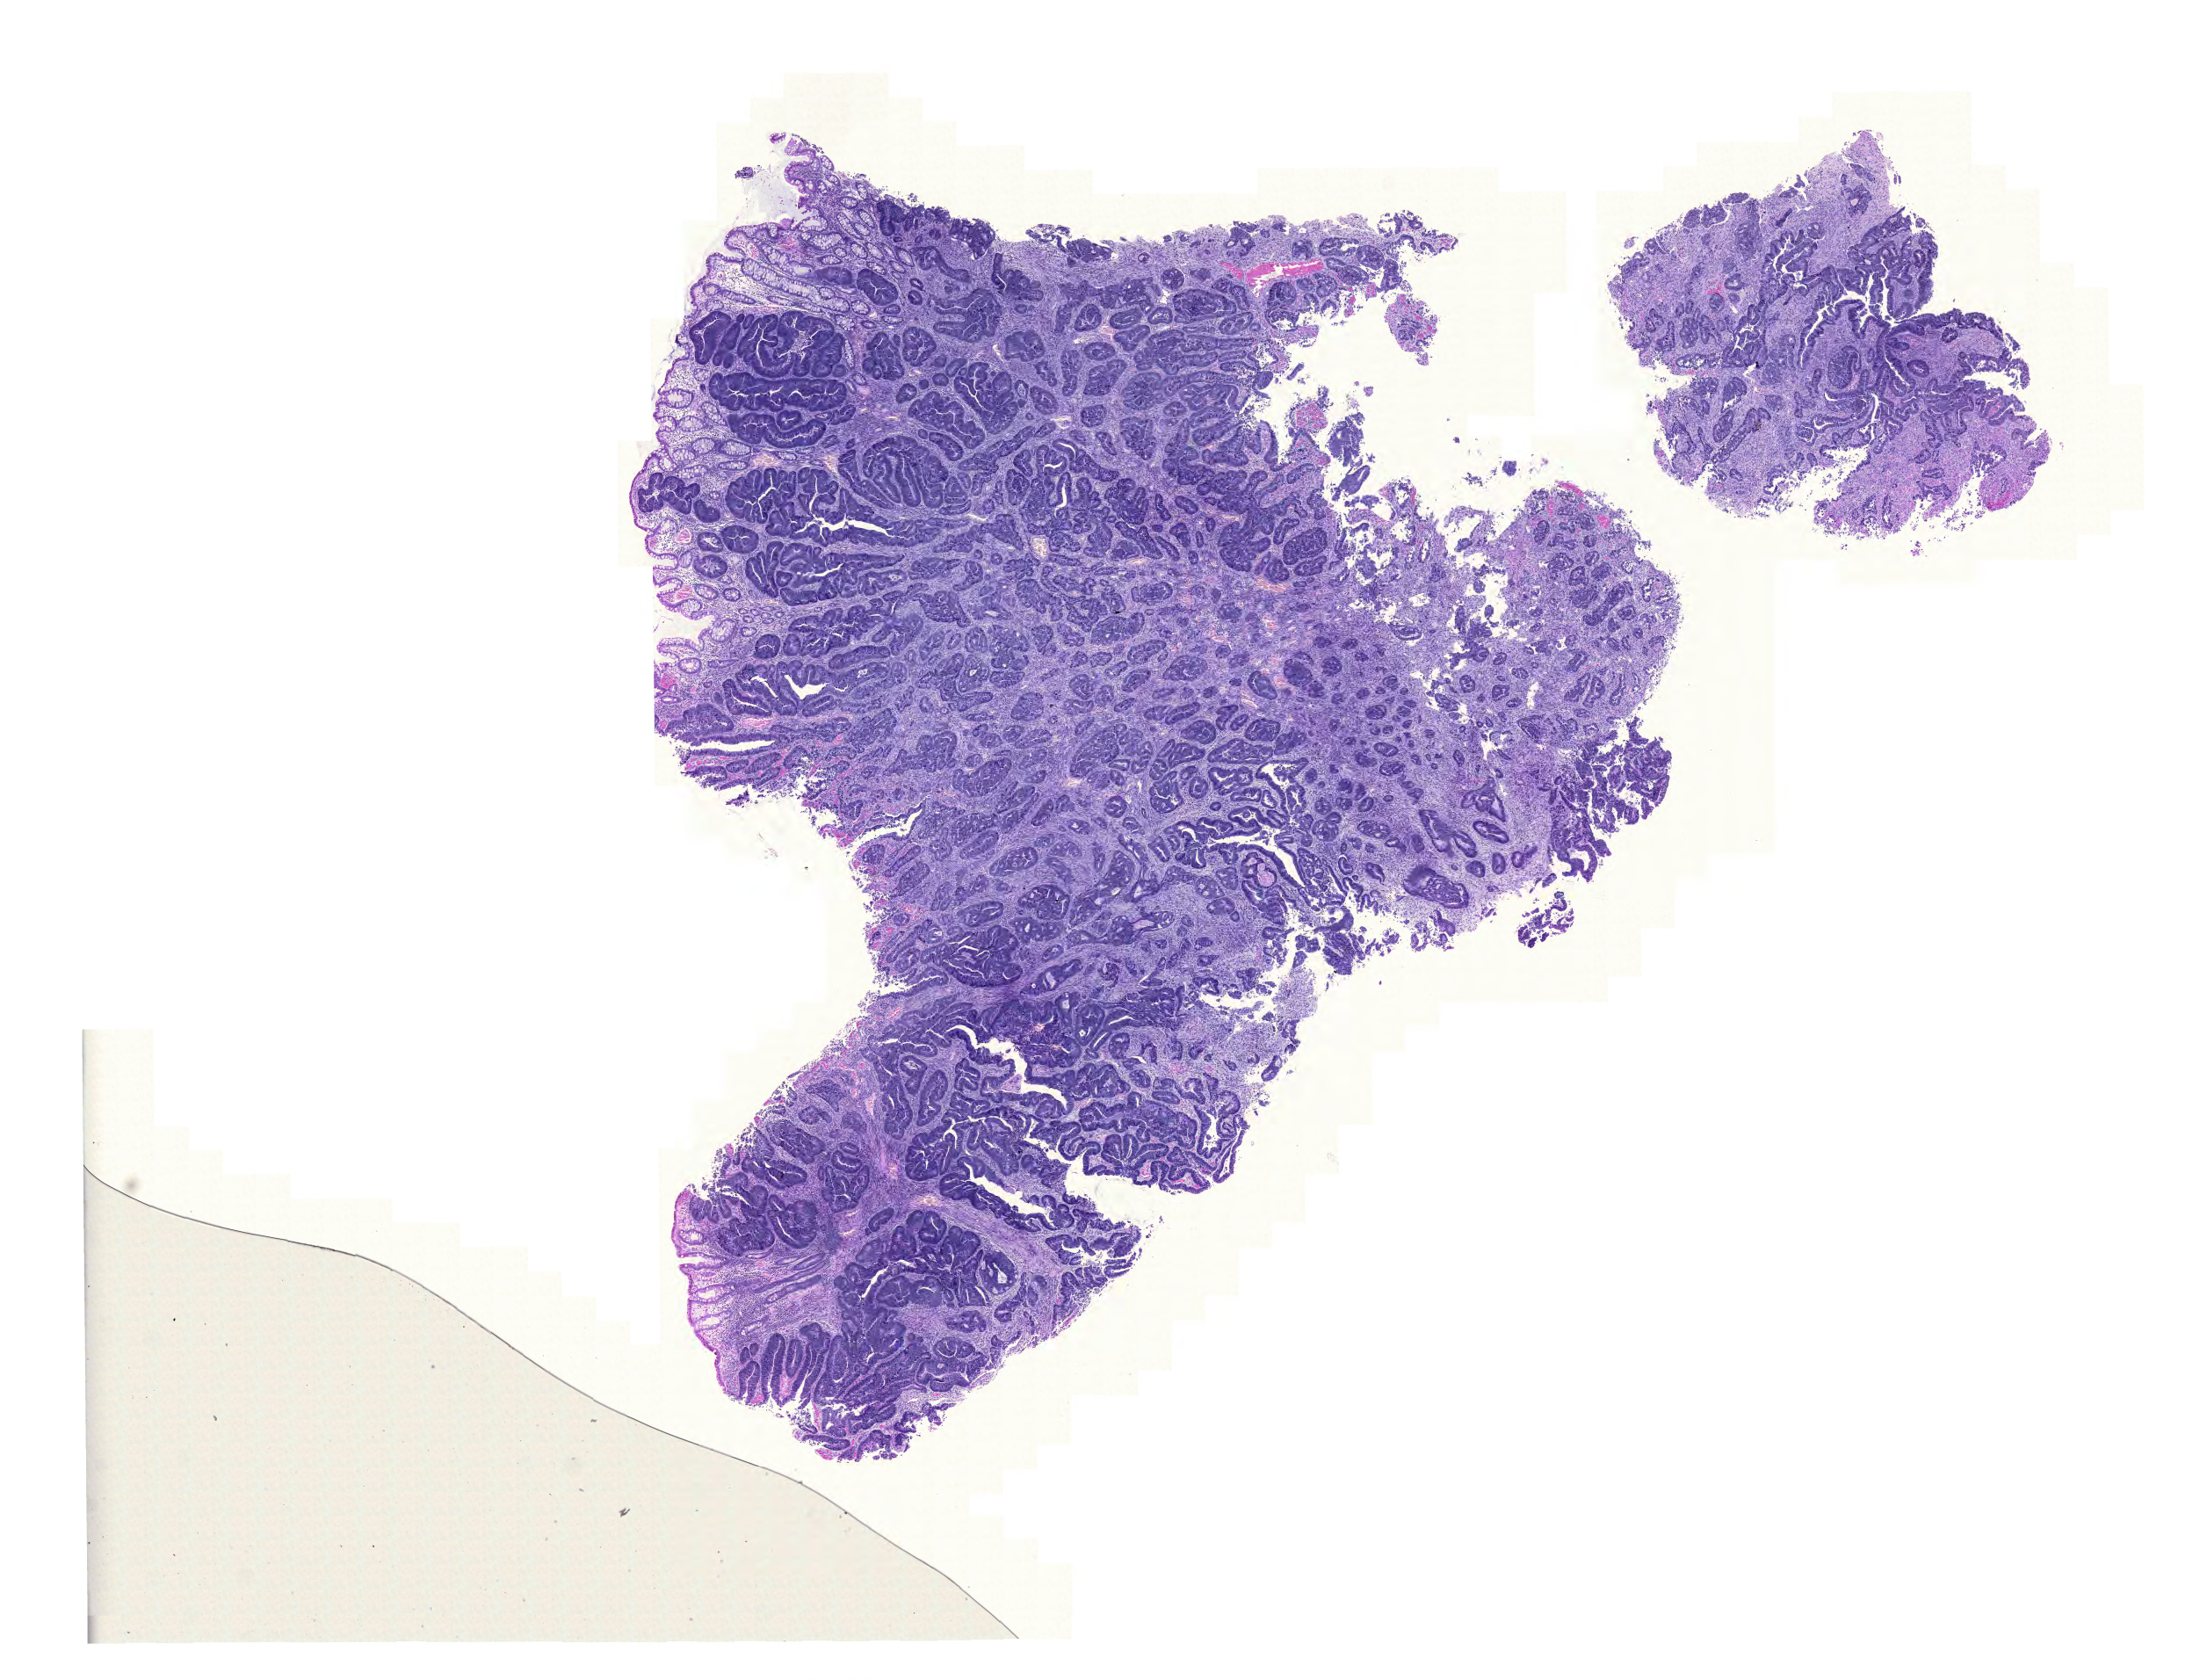
Whole-slide histology image, H&E, low-resolution overview of the scanned area, about 18.6 x 14.2 mm (acquisition: 20x scan), formalin-fixed paraffin-embedded (FFPE) diagnostic section, colon, primary tumour sample. Male, age 82 years at initial diagnosis.
AJCC pathologic stage: IIIC. Diagnosis: Adenocarcinoma, NOS. Lymph nodes positive (case pathology): 7 of 28 examined.